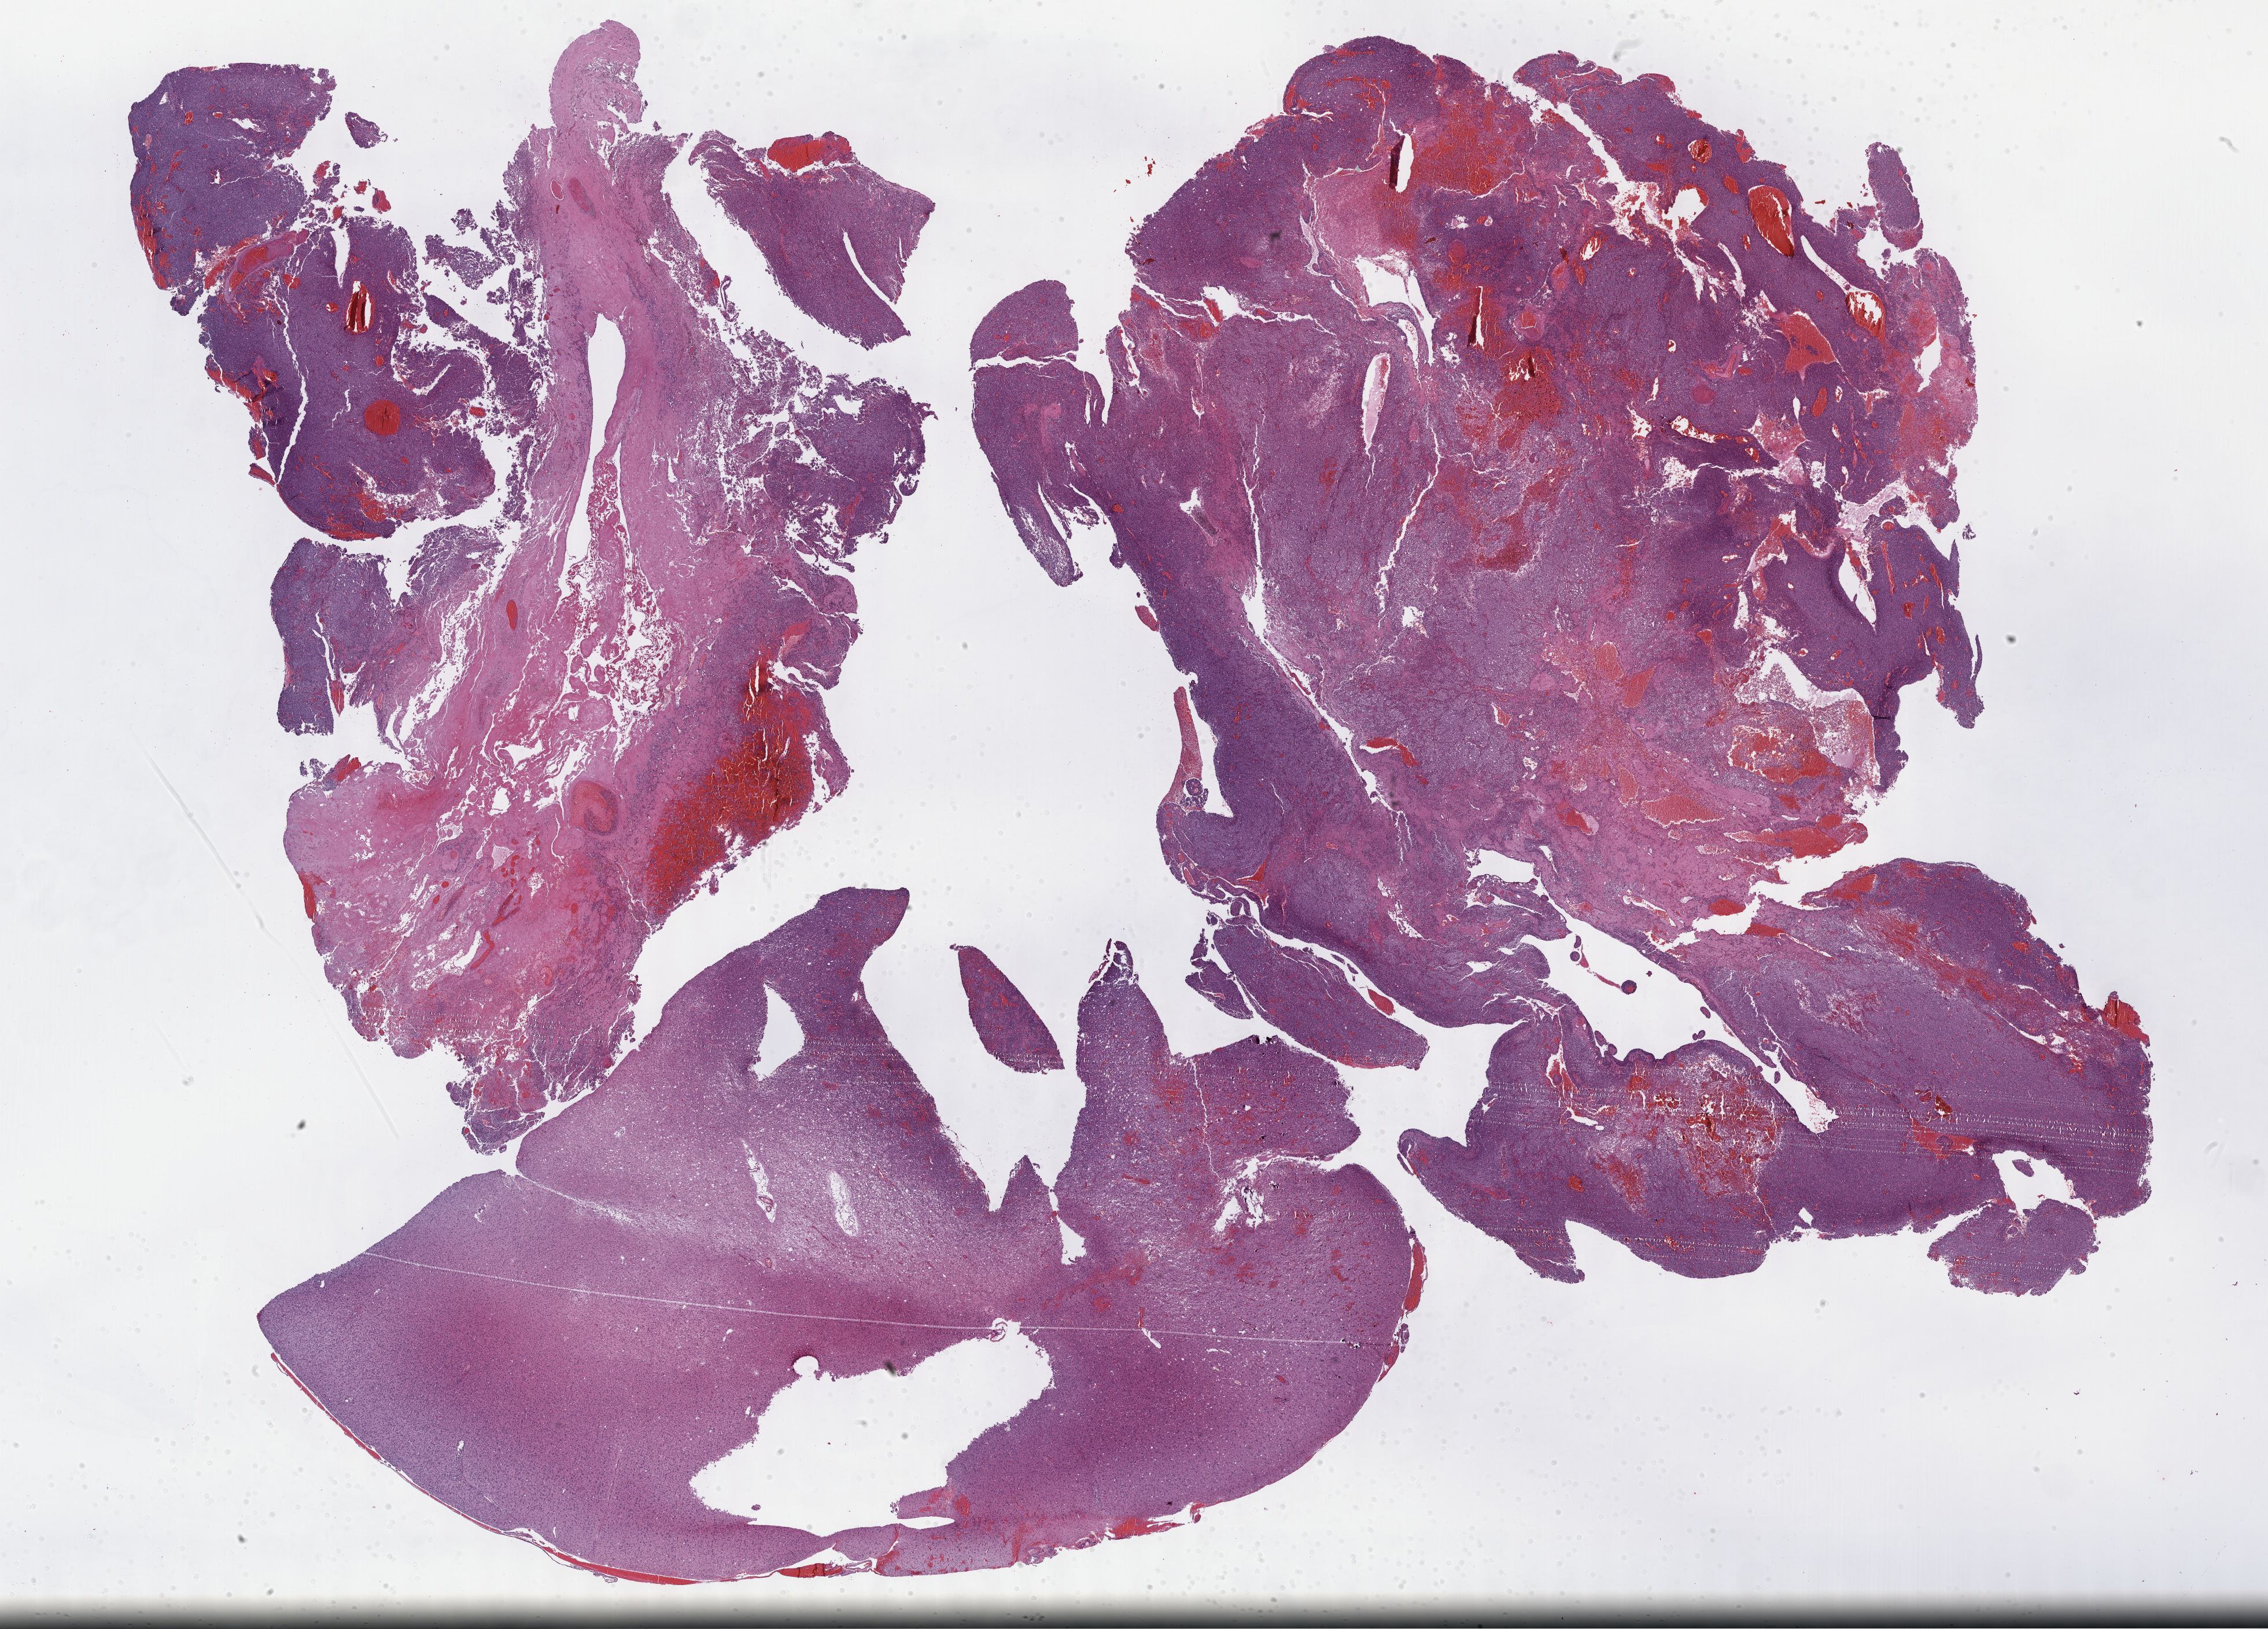
Whole-slide histology image, Hematoxylin and eosin (H&E) stained, a low-resolution overview of the entire scanned area, about 31.7 x 22.8 mm (from a 40x scan); formalin-fixed paraffin-embedded (FFPE) diagnostic section; brain, primary tumour sample. Male, age 33 years at initial diagnosis.
Pathologic diagnosis: Oligodendroglioma, anaplastic (cerebrum).